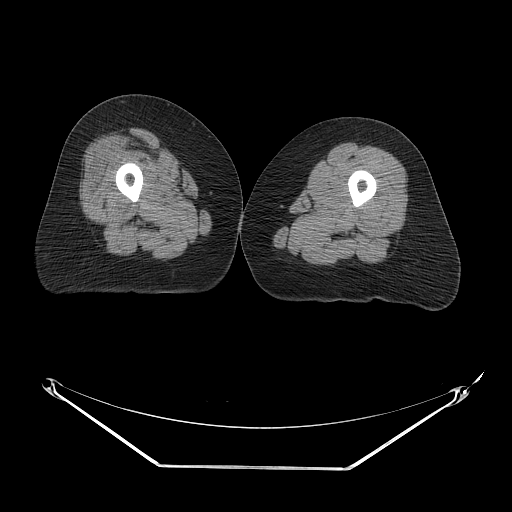
CT of an extremity soft-tissue mass (from a PET/CT study), one axial slice; position 16 of 267 along the scan axis; reconstruction kernel STANDARD; 140 kVp; soft-tissue window (W 400 / L 40 HU); 3.75 mm slice thickness; 512 × 512 image matrix, field of view 500 × 500 mm. Female patient. Case-level facts recorded for this patient, not image findings: histological type: malignant solitary fibrous tumor; grade: intermediate; site of the primary tumour: right thigh.
Outlined on this slice (expert contour drawn on MRI and transferred to this co-registered scan by the dataset authors):
- gross tumour volume including surrounding oedema: bounding box <126,130,181,168> (left, top, right, bottom; pixels)